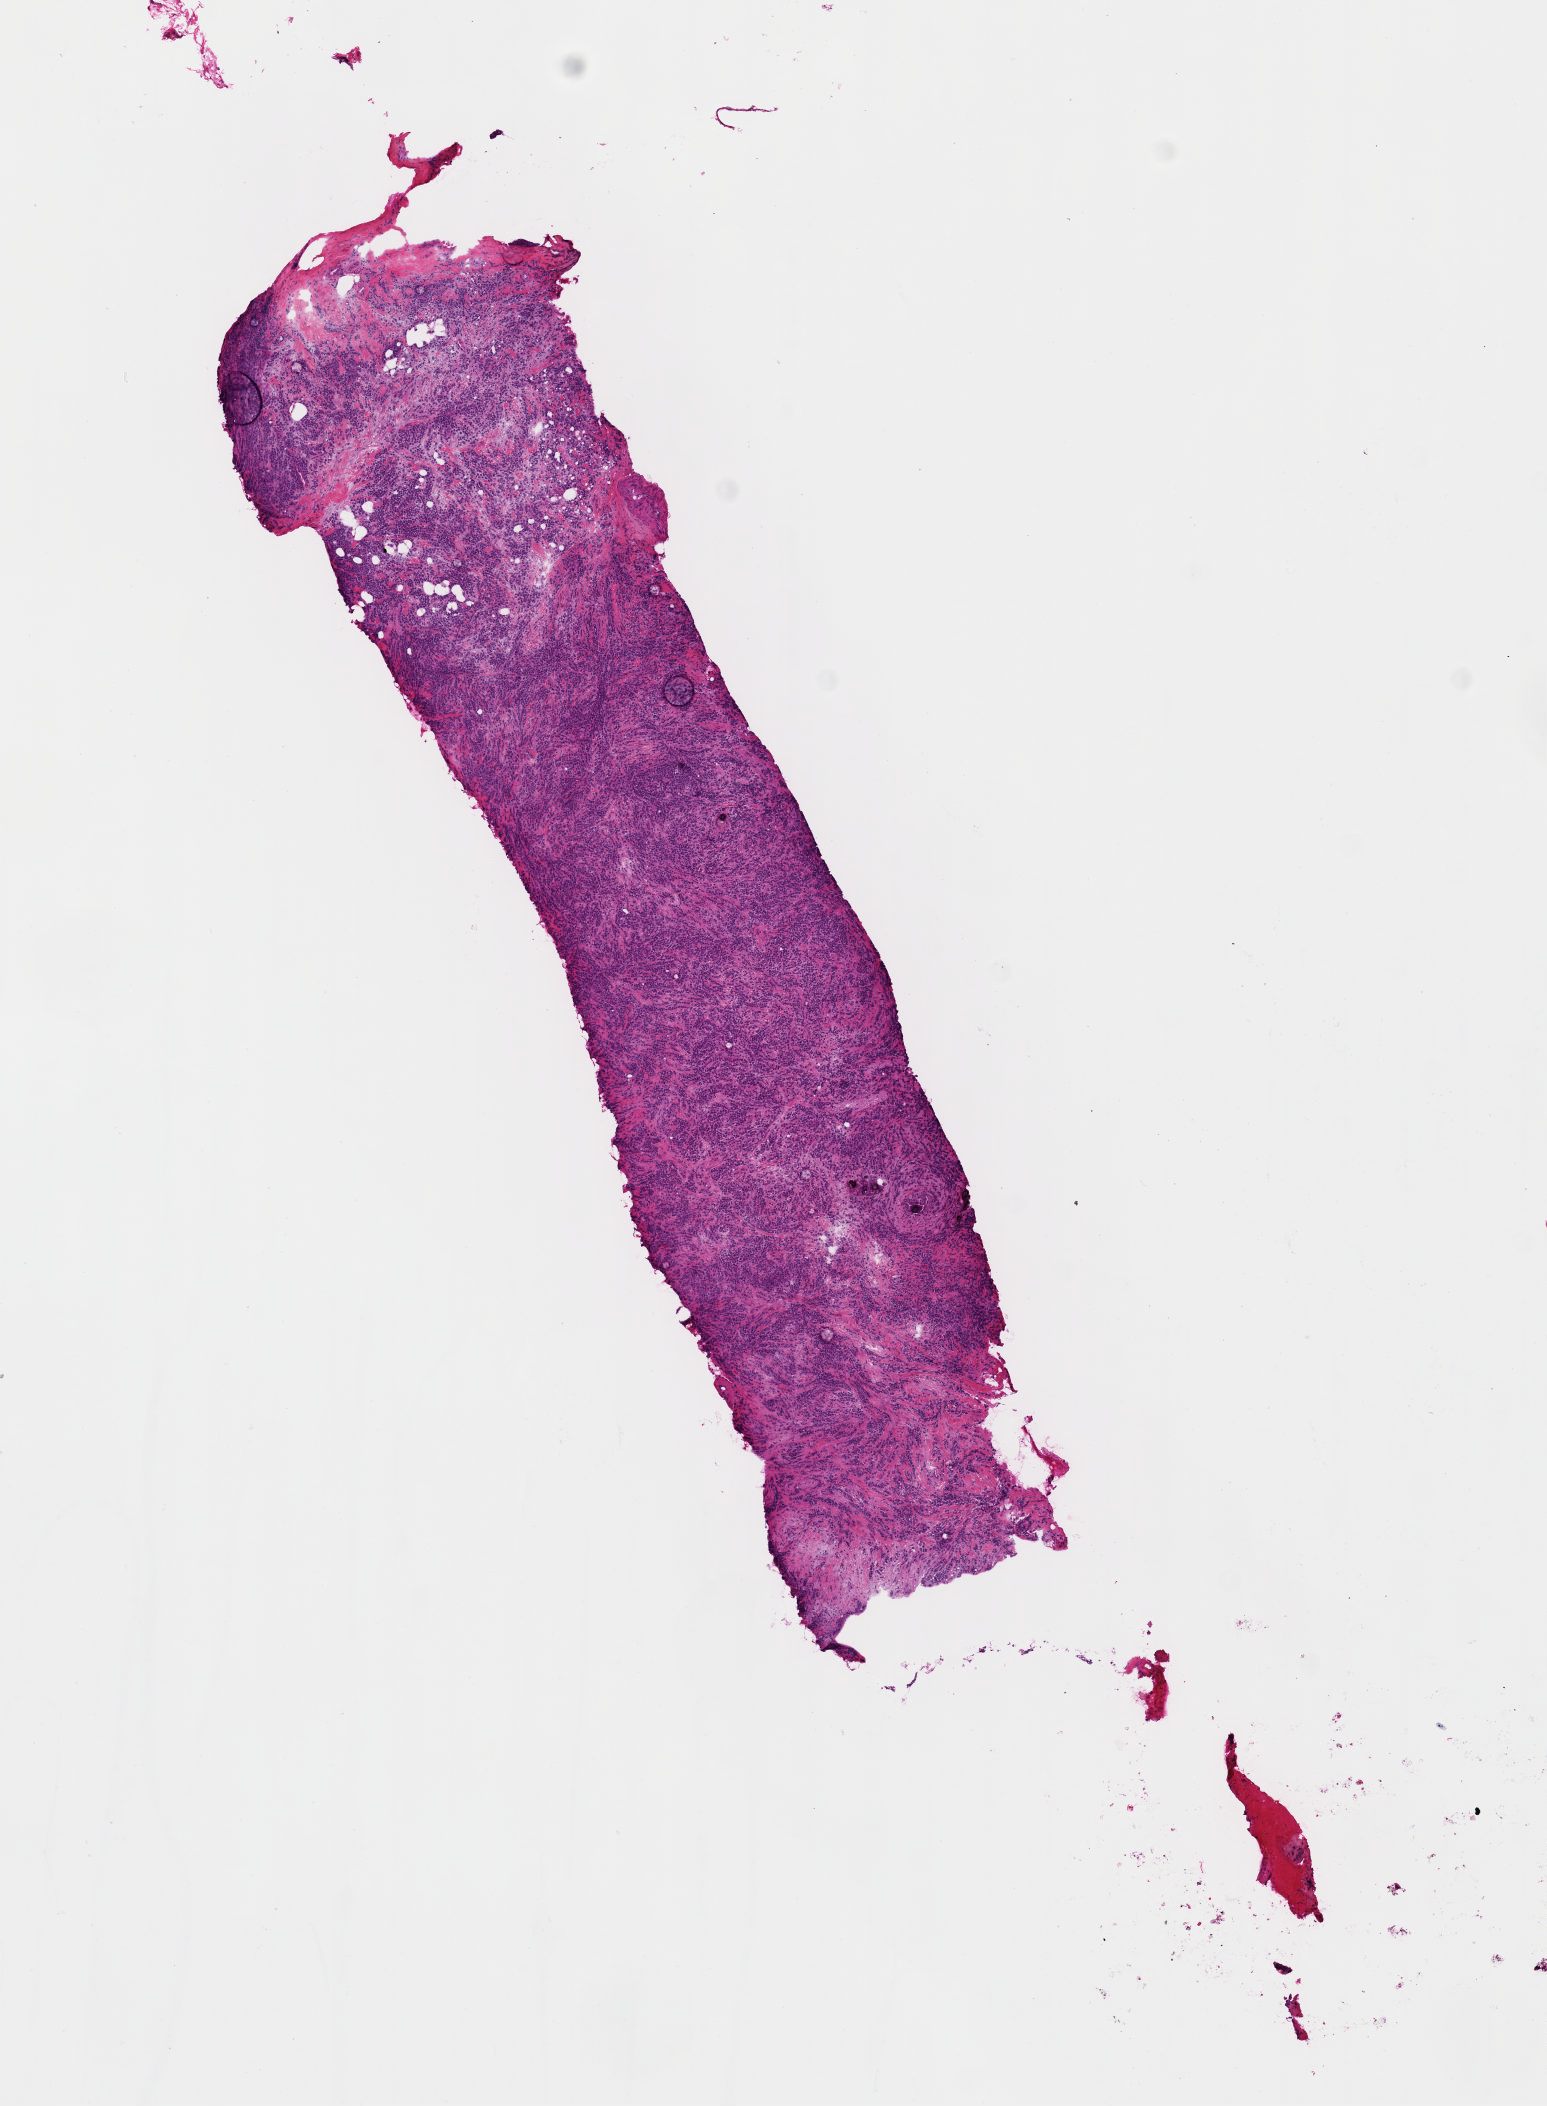
Whole-slide histology image, H&E-stained, low-resolution overview of the scanned area, about 6.1 x 8.3 mm. Frozen section from the top of the tissue portion. Primary tumour sample from the breast. Female patient; age at initial diagnosis 51 years. Composition of this section per pathologist review: tumour cells 80%, tumour nuclei 80%.
Pathologic diagnosis: Lobular carcinoma, NOS.